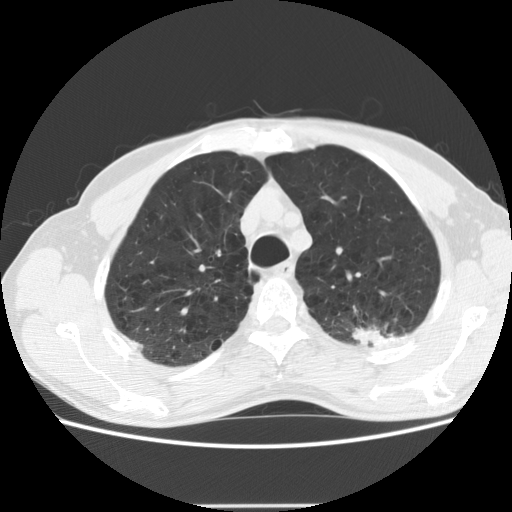
Low-dose screening chest CT, axial slice; first (baseline) screen; lung window (W 1500 / L -600 HU); 2.5 mm slice thickness; slice 39 of 191 in the series; 512 × 512 image matrix, field of view 352 × 352 mm. Male, age 64 years at enrolment.
Expert-annotated lung lesion, box from (x=341, y=290) to (x=426, y=359) px. Reader record for this screening exam (exam-level; its link to the box is not recorded): non-calcified nodule or mass ≥4 mm, left upper lobe, 27 × 19 mm, poorly defined margins, soft tissue attenuation. Later outcome: lung cancer diagnosed 23 days after this screen — adenocarcinoma, NOS, left upper lobe, moderately differentiated (G2), stage IA (AJCC 6th edition), 29 mm at pathology.